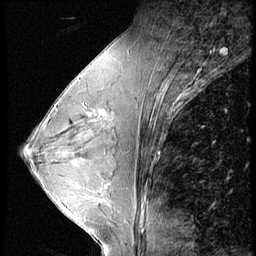
Breast MRI (dynamic contrast-enhanced), one sagittal slice. Slice 33 of 56 in the series (ordered by position). 4 images stored at this slice position (order not interpretable as contrast timing). 1.5 T. TE 4.2 ms, TR 9 ms. 256 × 256 image matrix, field of view 180 × 180 mm. Patient: female, 45 years. From the clinical record (not read from this slice): setting: breast cancer imaged before/during neoadjuvant chemotherapy; receptor status: triple-negative.
Outlined on this slice (semi-automatic segmentation, software-assisted and operator-edited):
- analysis volume of interest (the breast-tissue region the enhancement analysis was run in; not a lesion): bounding box (x1, y1, x2, y2) in pixels: (77, 104, 97, 124)
- tumour enhancement mask (voxels above the 140 % enhancement threshold inside the analysis volume of interest): (77, 104, 97, 123)